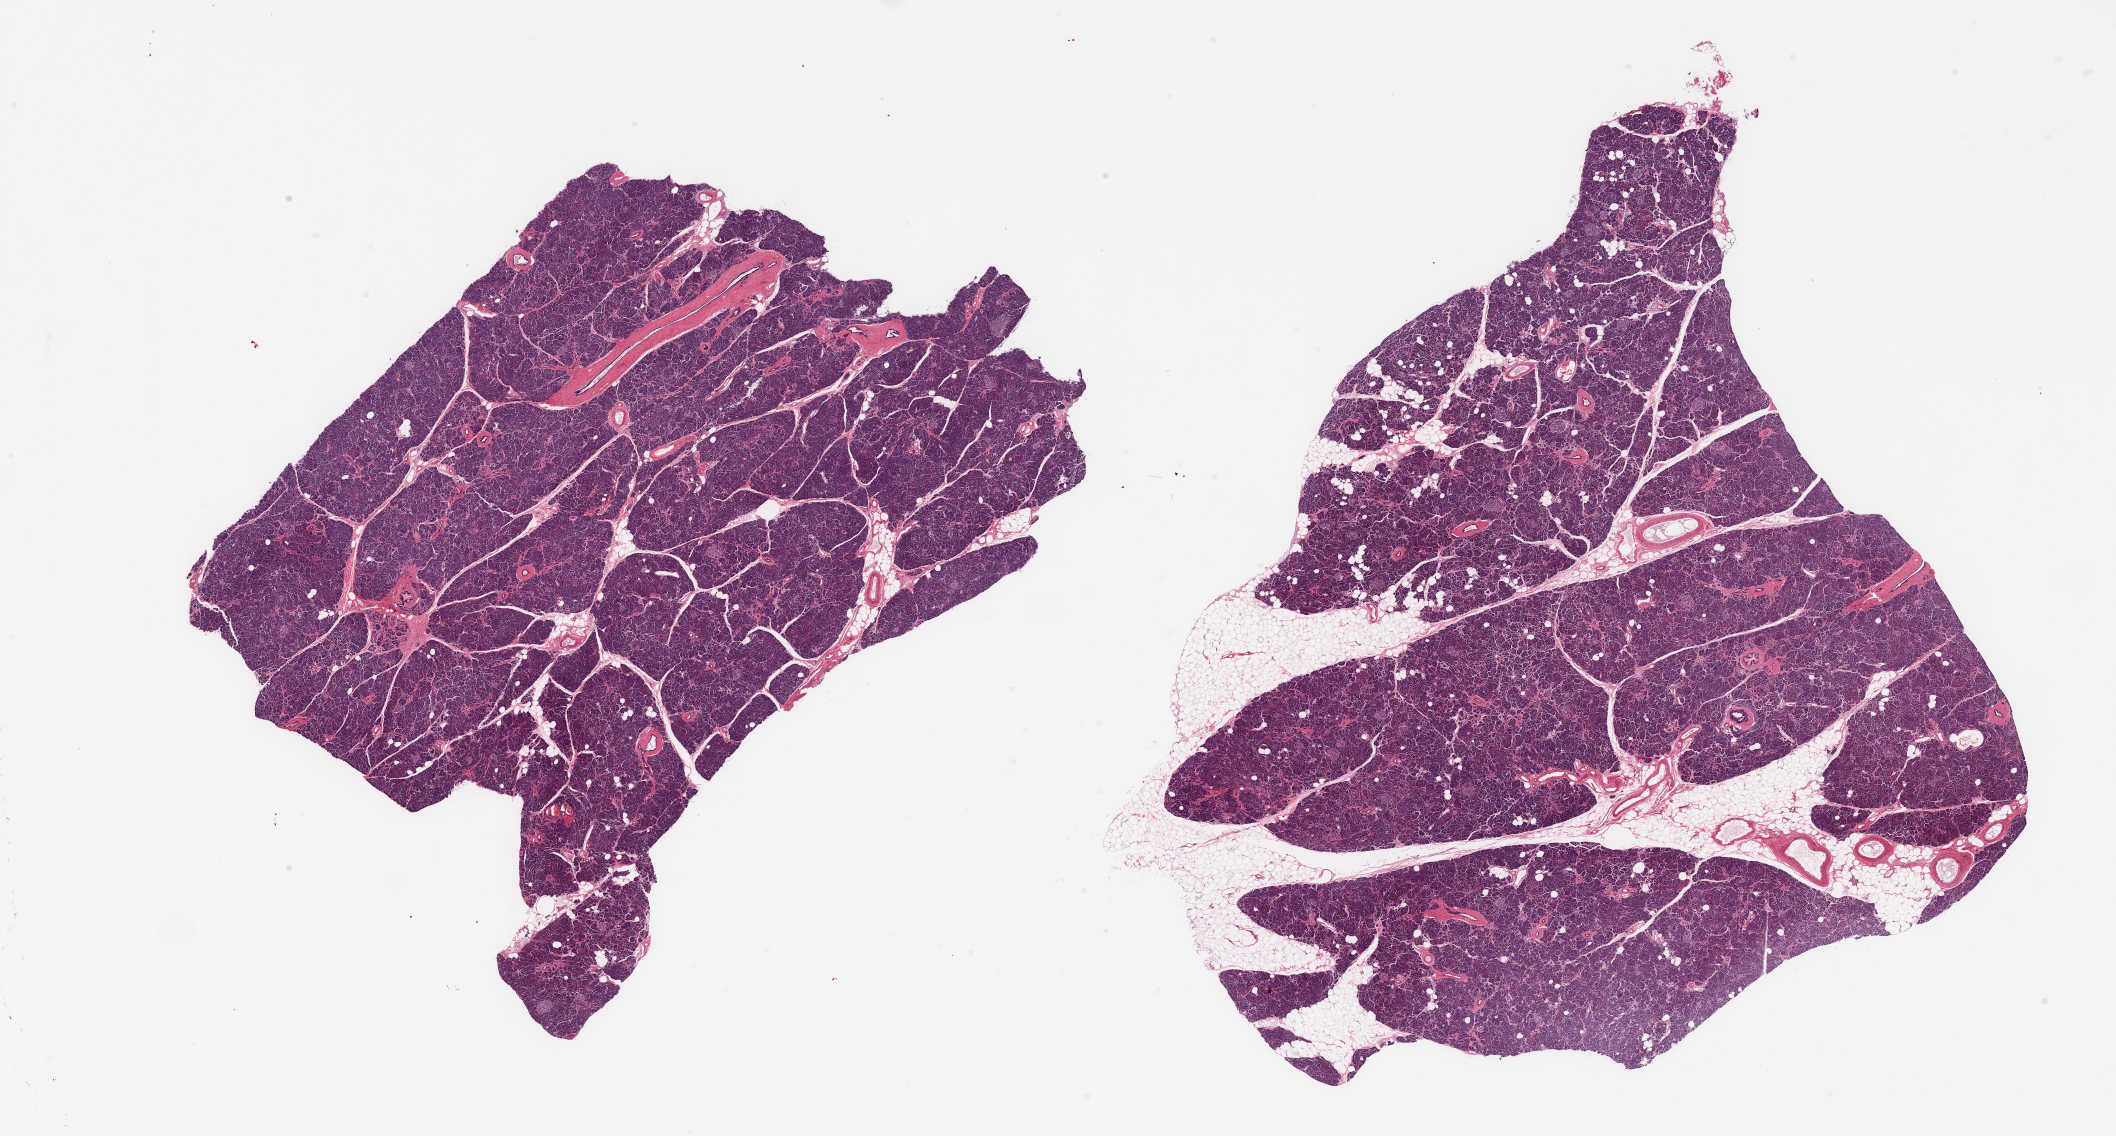
Digitized haematoxylin and eosin-stained section — a low-resolution overview of the entire scanned area, about 33.5 x 18.0 mm (slide scanned at 20x); PAXgene-fixed, paraffin-embedded tissue; target tissue: pancreas; tissue donor sample. Male donor.
Reviewer comment on this tissue sample: 2 pieces, Islets moderately abundant, well-preserve.